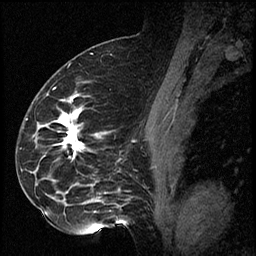
Breast MRI (dynamic contrast-enhanced), one sagittal slice; position 41 of 60 along the scan axis; dynamic contrast-enhanced series, image 2 of 2 at this slice position (ordered by acquisition); 1.5 T; TE 4.2 ms, TR 17.3 ms; 2 mm slice thickness; 256 × 256 image matrix, field of view 200 × 200 mm. Female patient. From the clinical record (not read from this slice): setting: breast cancer imaged before/during neoadjuvant chemotherapy; receptor status: HR-positive, HER2-negative.
Outlined on this slice (semi-automatically segmented with operator editing):
- analysis volume of interest (the breast-tissue region the enhancement analysis was run in; not a lesion): bounding box (x1, y1, x2, y2) in pixels: (41, 93, 115, 223)
- tumour enhancement mask (voxels above the 100 % enhancement threshold inside the analysis volume of interest): (63, 111, 82, 157)